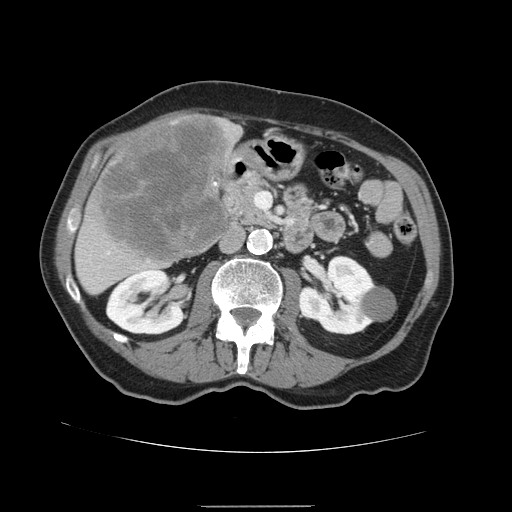
Contrast-enhanced abdominal CT, one axial slice; slice 60 of 168 in the series (ordered by position); 120 kVp; intravenous contrast given; soft-tissue window (W 400 / L 40 HU); 512 × 512 image matrix, field of view 386 × 386 mm. Male patient, age 74 years. From the clinical record (not read from this slice): diagnosis: colorectal cancer liver metastases, imaged before liver resection; multiple liver metastases: no; largest metastasis: 14.5 cm; disease in both lobes: yes.
Structures marked on this image (expert manual segmentation):
- liver: box from (x=75, y=111) to (x=243, y=295) px
- liver metastasis: (x=94, y=117)–(x=231, y=264)